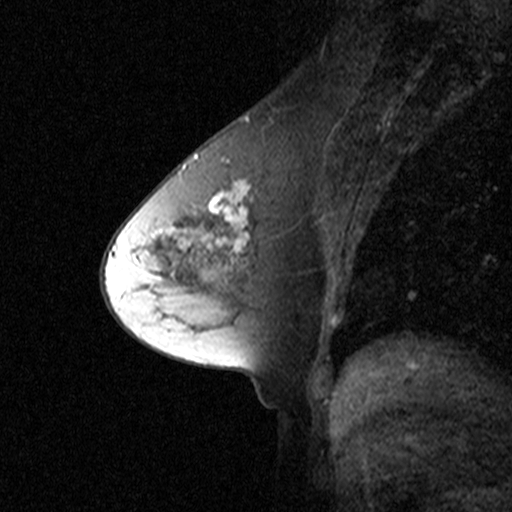
Breast MRI (dynamic contrast-enhanced), one sagittal slice. Slice 22 of 44 in the series (ordered by position). Dynamic contrast-enhanced study with each time point stored as its own series, time point 2 of 3 at this slice position (early post-contrast, ordered by acquisition time). 1.5 T. TE 4.5 ms, TR 11 ms. 3 mm slice thickness. 512 × 512 image matrix, field of view 200 × 200 mm. Female patient, age 53 years. Case-level facts recorded for this patient, not image findings: setting: breast cancer imaged before/during neoadjuvant chemotherapy; receptor status: HR-positive, HER2-negative.
Annotated regions visible in this slice (semi-automatic segmentation, software-assisted and operator-edited):
- analysis volume of interest (the breast-tissue region the enhancement analysis was run in; not a lesion): box from (x=170, y=150) to (x=277, y=273) px
- tumour enhancement mask (voxels above the 90 % enhancement threshold inside the analysis volume of interest): (x=179, y=154)–(x=251, y=251)